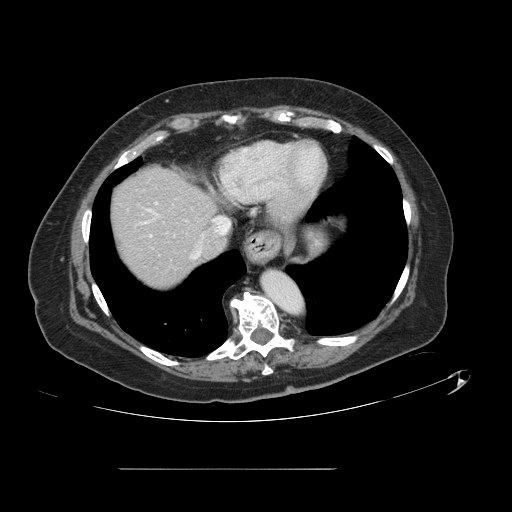
Contrast-enhanced abdominal CT, one axial slice; position 118 of 148 along the scan axis; 120 kVp; intravenous contrast given; soft-tissue window (W 400 / L 40 HU); 2.5 mm slice thickness; 512 × 512 image matrix, field of view 439 × 439 mm. Female patient, age 75 years. Case-level facts recorded for this patient, not image findings: diagnosis: colorectal cancer liver metastases, imaged before liver resection; multiple liver metastases: no; largest metastasis: 2.4 cm; disease in both lobes: no.
Annotated regions visible in this slice (outlined manually by an expert reader):
- hepatic veins: box from (x=191, y=217) to (x=230, y=259) px
- liver: (x=110, y=168)–(x=214, y=289)
- planned liver remnant (the part of the liver to remain after resection): (x=110, y=168)–(x=214, y=289)